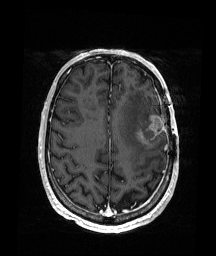
Brain MRI from a brain-tumour surgery series, one axial slice. Slice 64 of 176 in the series (ordered by position). T1-weighted post-contrast. 216 × 256 image matrix, field of view 219 × 260 mm. Case-level facts recorded for this patient, not image findings: histopathology: Glioblastoma; WHO grade: 4; IDH mutation: no; tumour location: Left Frontal.
Structures marked on this image (manually delineated by an expert):
- tumour: bounding box (x1, y1, x2, y2) in pixels: (135, 112, 167, 148)